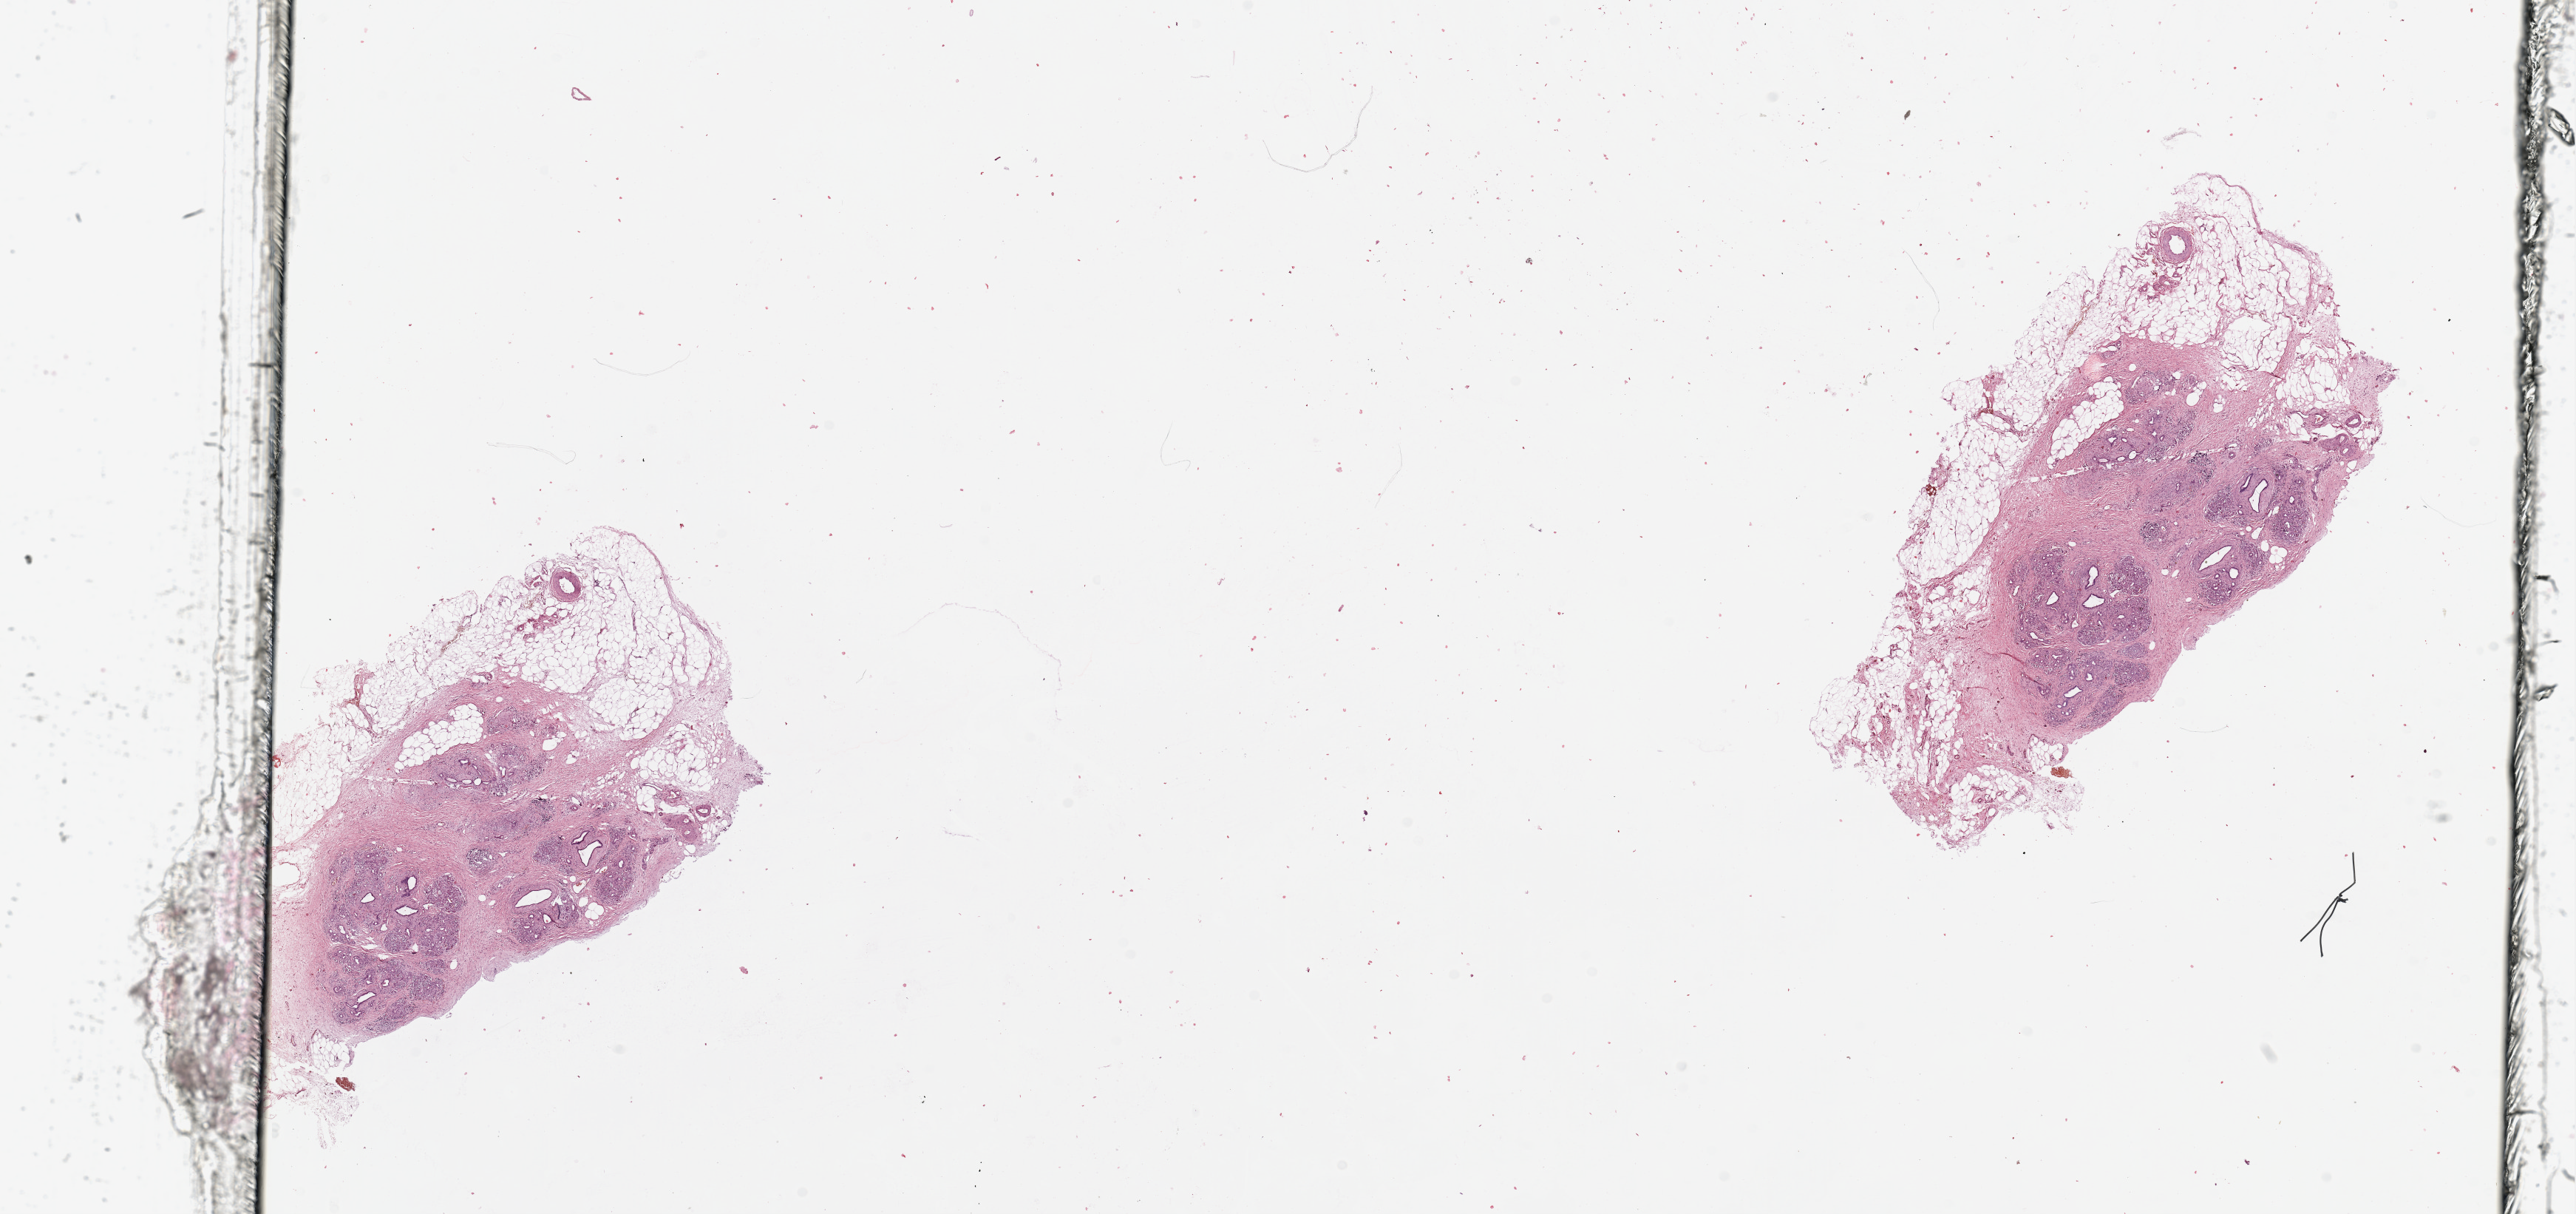
Hematoxylin and eosin (H&E) stained whole-slide image — a low-resolution overview of the entire scanned area, about 27.6 x 13.0 mm, pancreas, tissue type not recorded.
• patient diagnosis (cohort enrolment): ductal adenocarcinoma (pancreas)